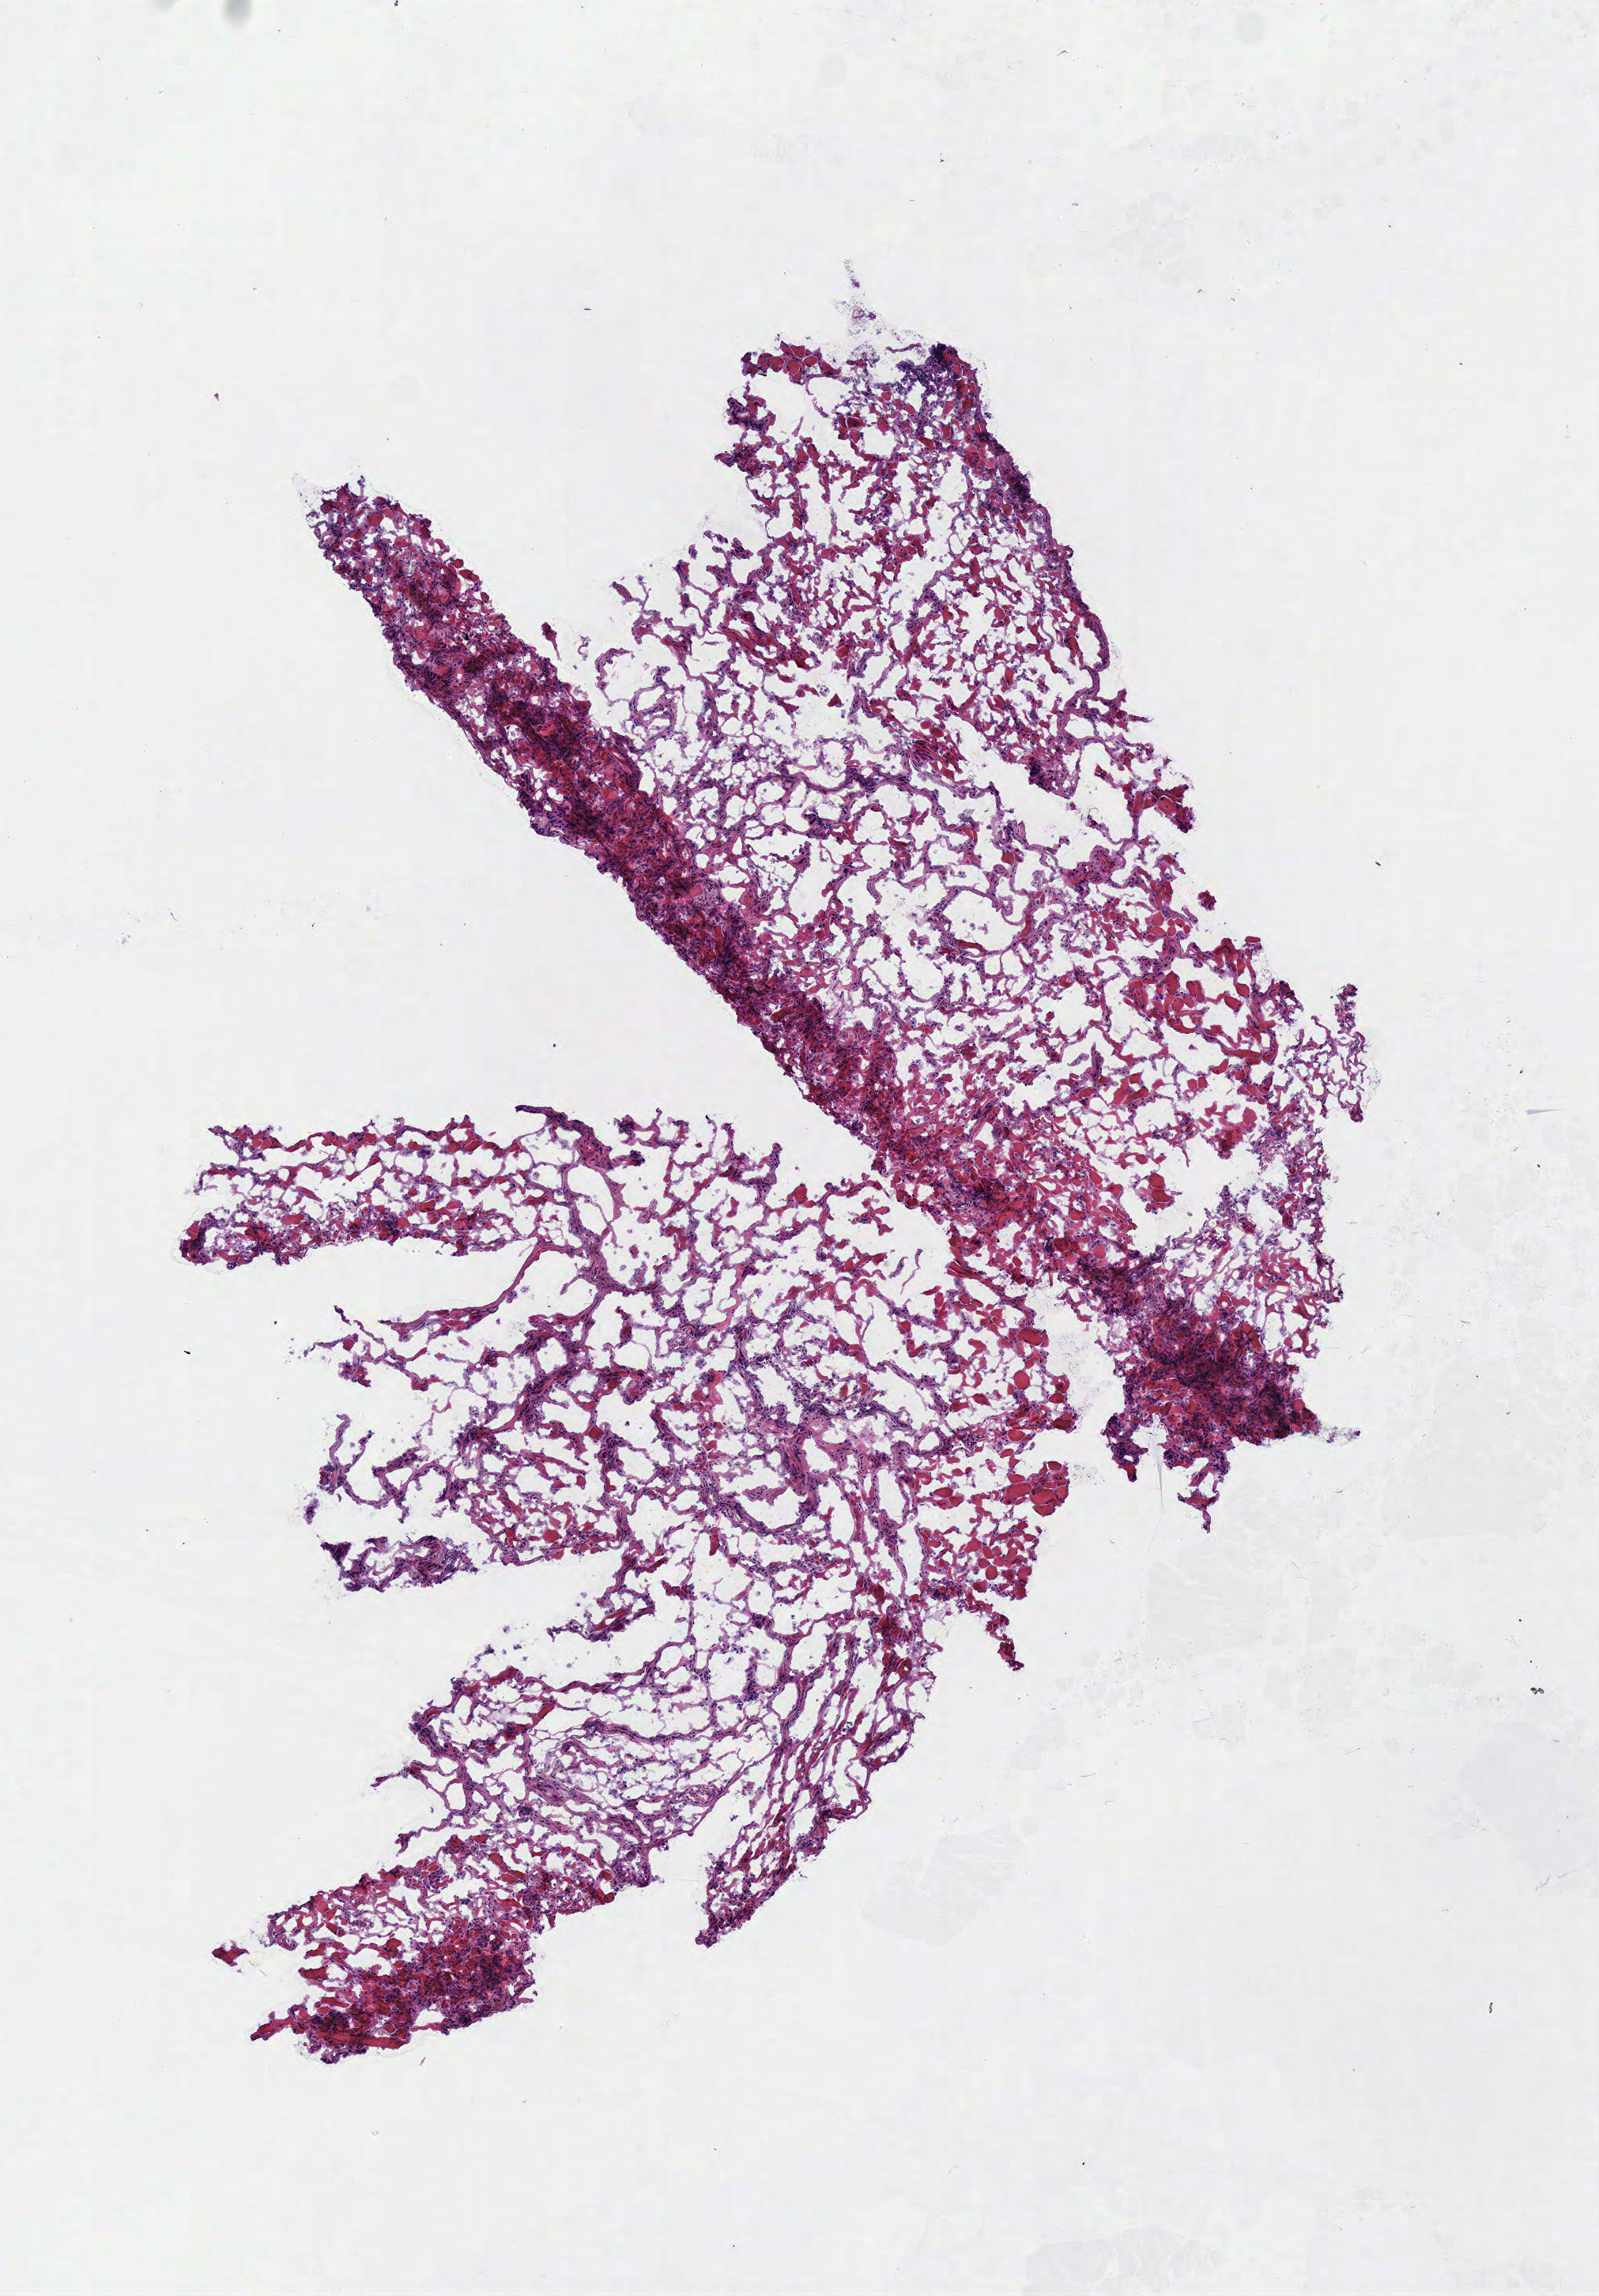
Whole-slide histology image, Hematoxylin and eosin (H&E) stained — whole scanned area (about 4.0 x 5.7 mm) shown as a low-resolution overview; frozen section from the top of the tissue portion; head and neck, primary tumour sample. Female patient; age at initial diagnosis 63 years. Histologic grade: G3 (poorly differentiated). Slide review estimates, as recorded: tumour cells 90%, tumour nuclei 80%, normal cells 0%, stromal cells 10%, necrosis 0%.
AJCC pathologic stage: IVA (7th edition). Pathologic diagnosis: Squamous cell carcinoma, NOS.